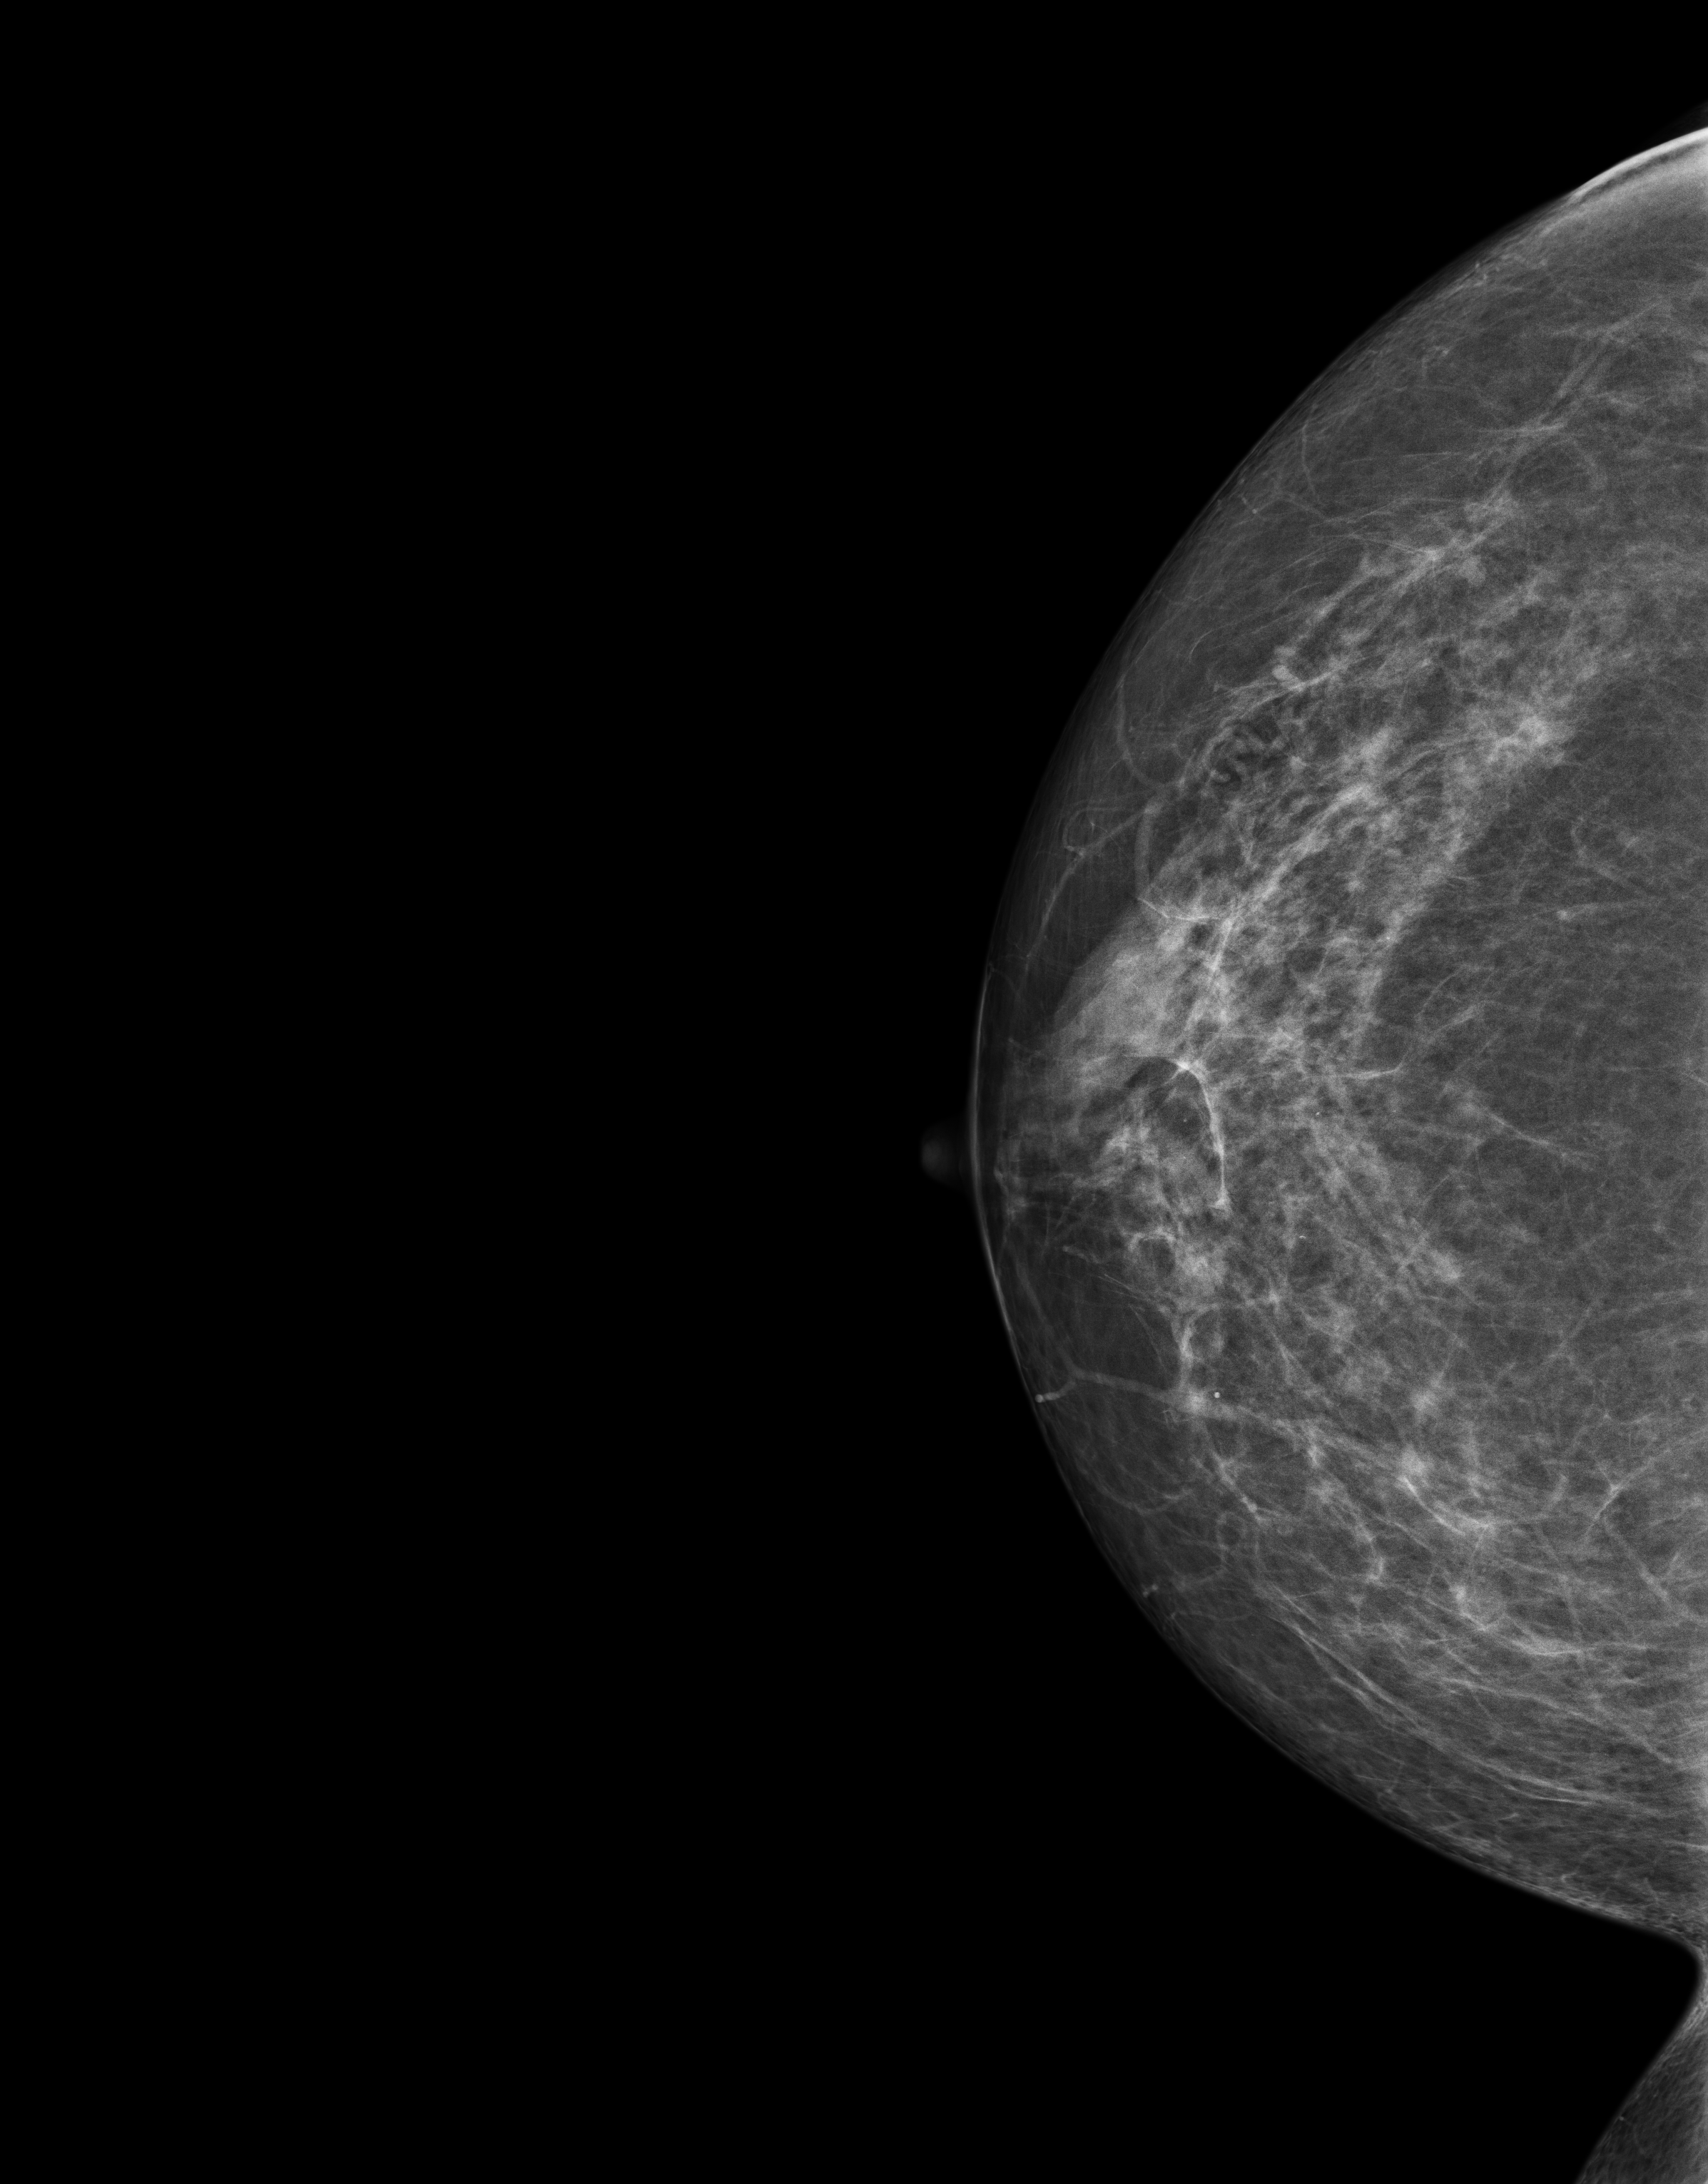
Digital mammogram (FFDM), right breast, cranio-caudal projection, annual screening mammography examination, system: Senographe Essential ADS_56.21.3. Patient: female, 53 years.
- breast density at the screening exam (both breasts): heterogeneously dense (BI-RADS density category c)
- final BI-RADS category for the screening round (tomosynthesis exam, both breasts): category 4
- recall: recalled for additional imaging after this screen